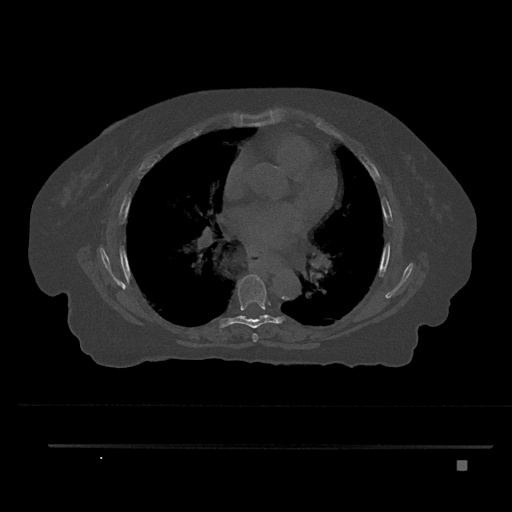
CT including the spine, one axial slice; position 489 of 797 along the scan axis; reconstruction kernel Br40s/3; 120 kVp; bone window (W 1800 / L 400 HU); 512 × 512 image matrix. Female patient, age 76 years. From the clinical record (not read from this slice): primary cancer: lung; vertebrae with lytic lesions (as recorded): T11, L3.
Outlined on this slice (semi-automatic segmentation, software-assisted and operator-edited):
- T6 vertebra: box from (x=252, y=333) to (x=258, y=342) px
- T7 vertebra: (x=220, y=274)–(x=285, y=328)
- T8 vertebra: (x=241, y=315)–(x=261, y=318)